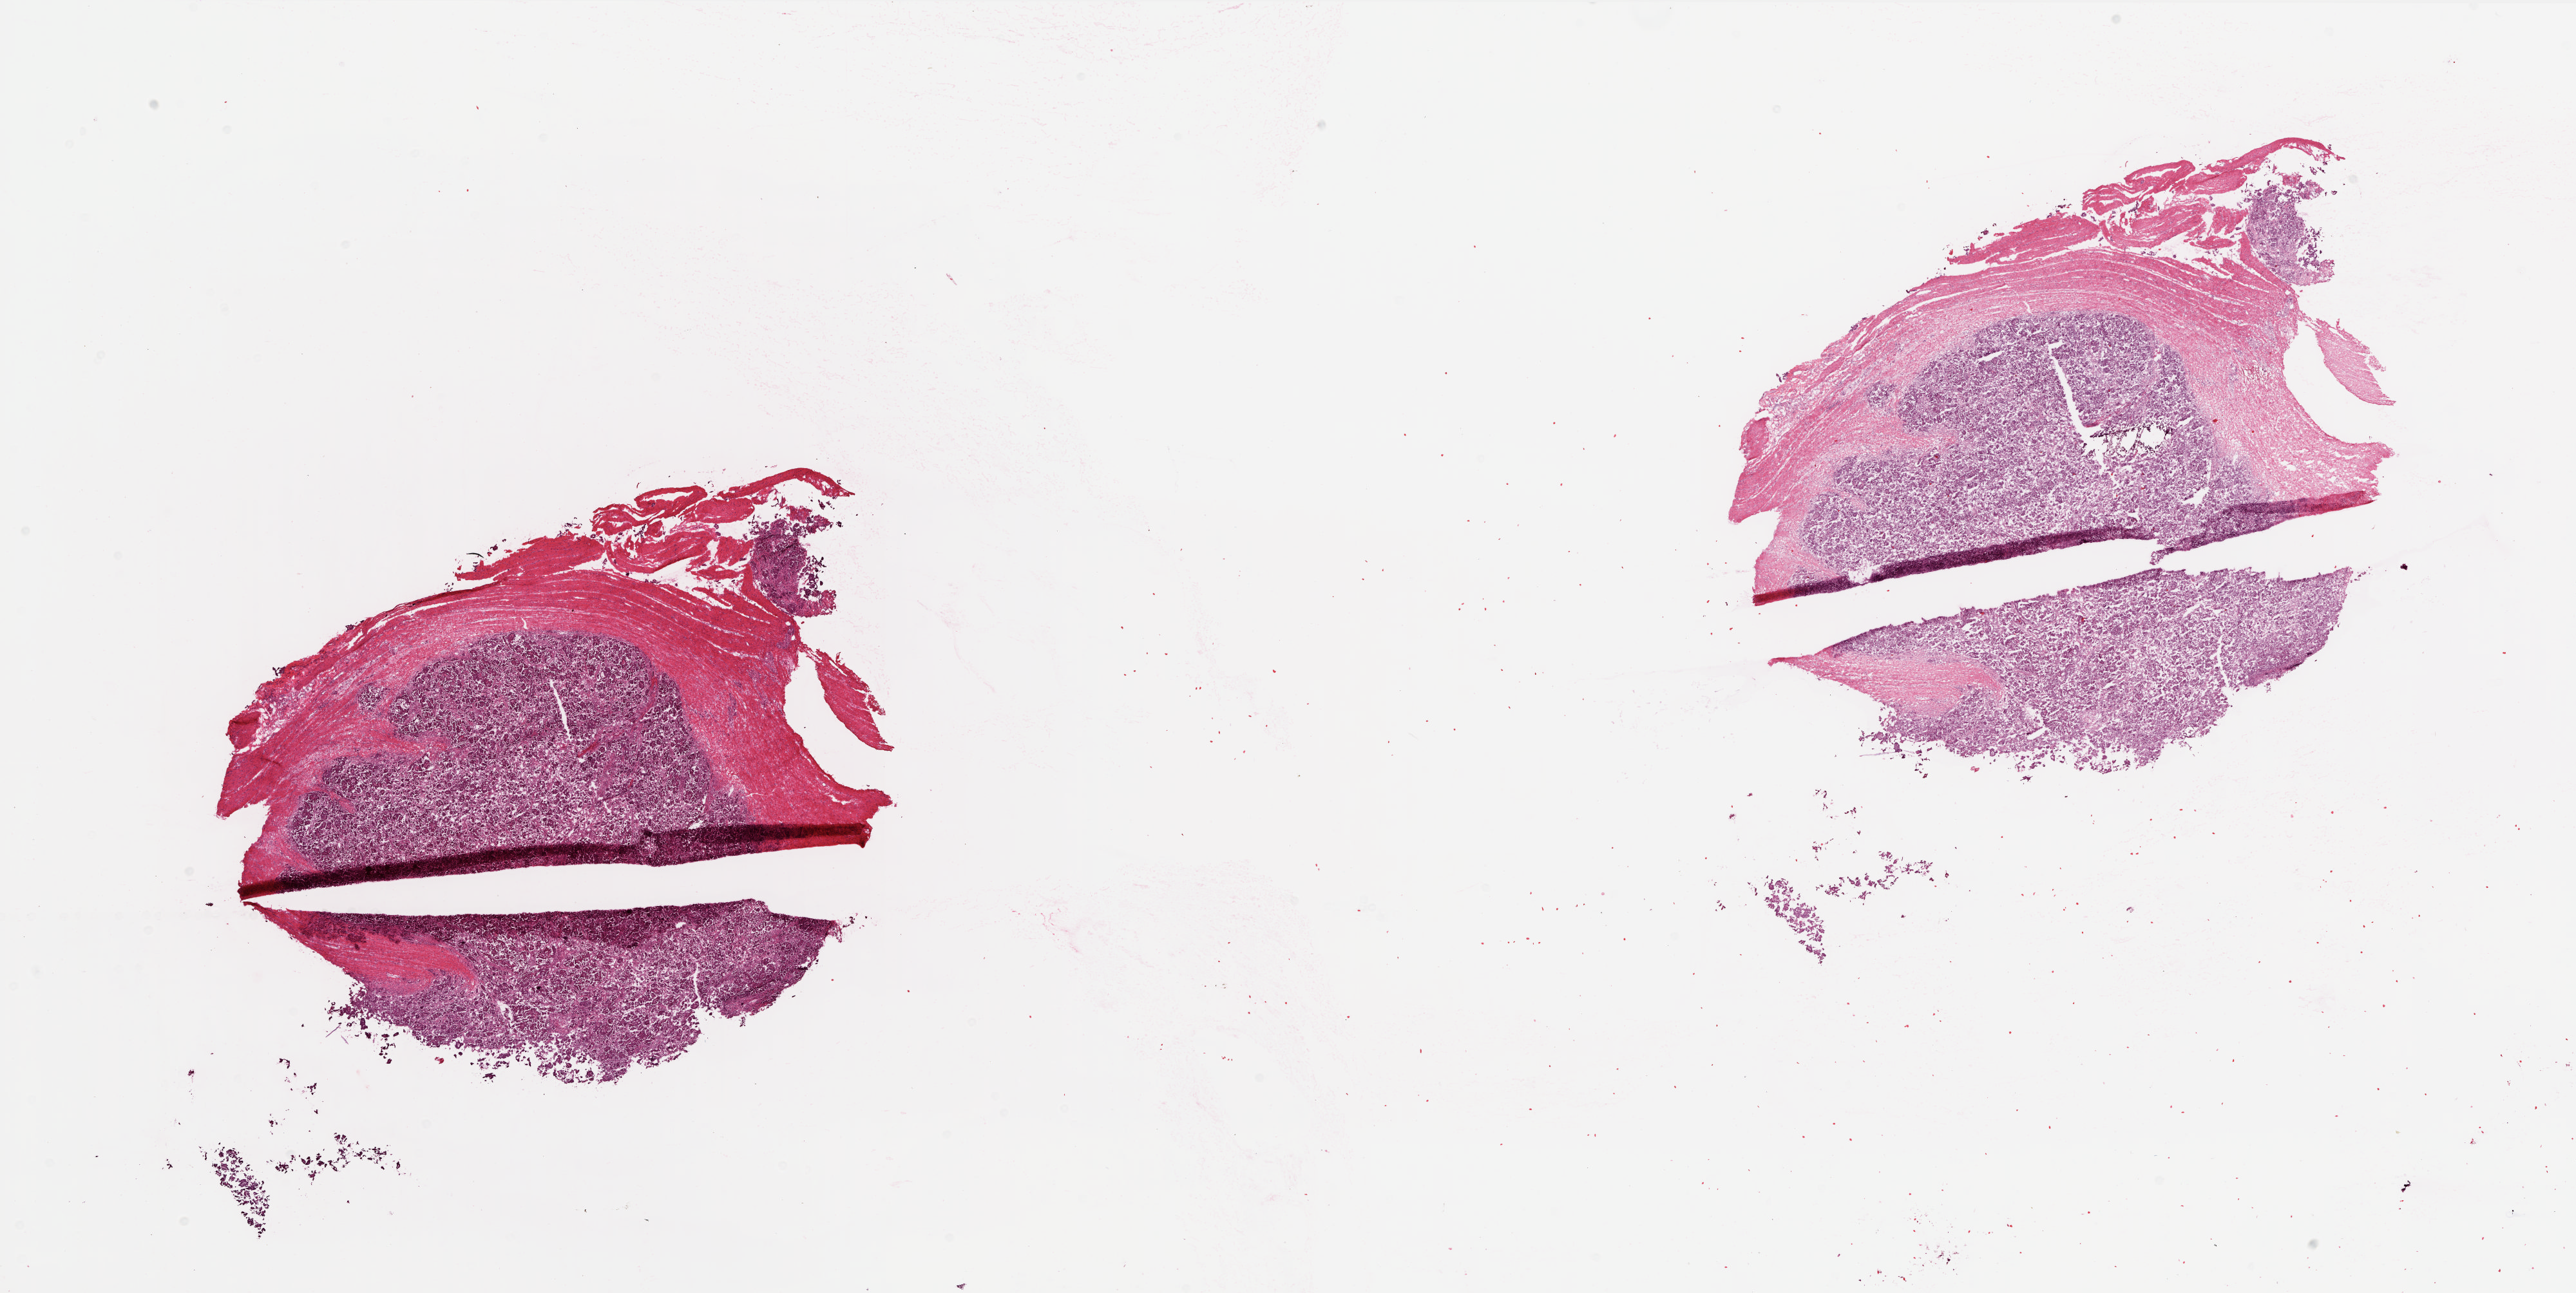
H&E-stained whole-slide image, a low-resolution overview of the entire scanned area, about 31.9 x 16.0 mm. Frozen section. Ovary, primary tumour sample. Patient: female, age at initial diagnosis 78 years. Histologic grade: G2 (moderately differentiated). Pathologist review of this section (percent, as recorded): tumour cells 79%, tumour nuclei 82%, normal cells 0%, stromal cells 21%, necrosis 0%.
FIGO stage: IIIC. Histologic diagnosis: Serous cystadenocarcinoma, NOS.